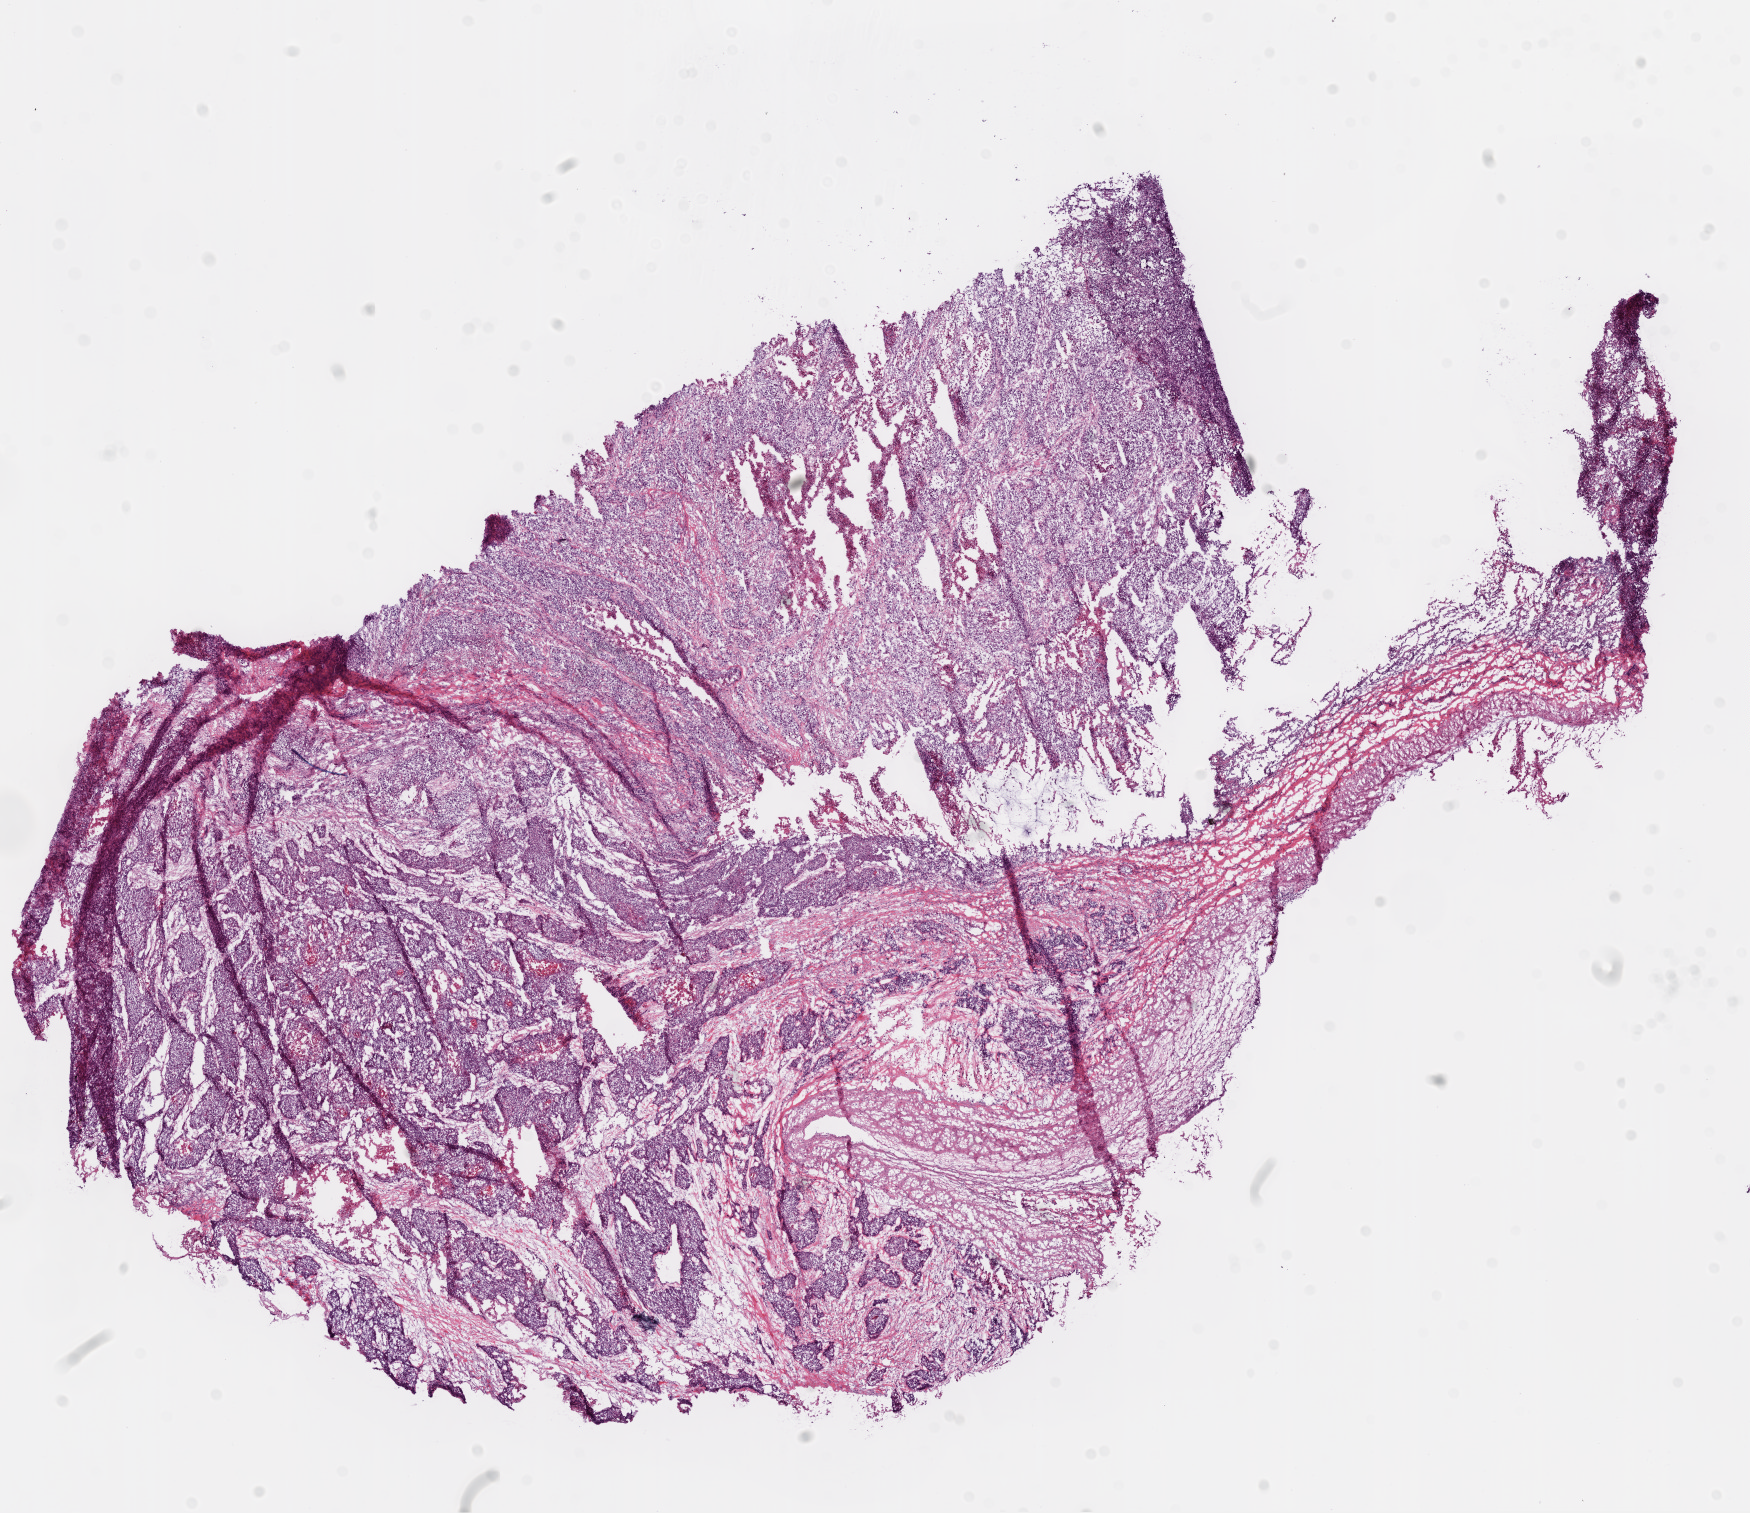
Digitized H&E tissue section (whole slide) — low-resolution overview of the scanned area, about 14.0 x 12.1 mm (acquisition: 20x scan); frozen section from the bottom of the tissue portion; sample: primary tumour, lung. Patient: male, age at initial diagnosis 62 years. Pathologist review of this section (percent, as recorded): tumour cells 70%, tumour nuclei 80%, normal cells 0%, stromal cells 20%, necrosis 10%.
- diagnosis: Squamous cell carcinoma, NOS (lower lobe, lung)
- laterality: right
- AJCC pathologic stage: IIB